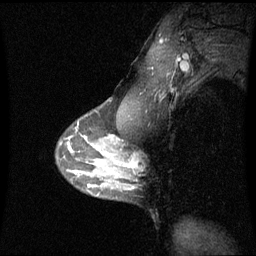
Breast MRI (dynamic contrast-enhanced), one sagittal slice; dynamic contrast-enhanced series, image 2 of 3 at this slice position (ordered by acquisition); 1.5 T; TE 4.2 ms, TR 8.9 ms; 256 × 256 image matrix, field of view 230 × 230 mm. Female patient, age 42 years. Case-level facts recorded for this patient, not image findings: setting: breast cancer imaged before/during neoadjuvant chemotherapy; receptor status: triple-negative.
Annotated regions visible in this slice (semi-automatic segmentation, software-assisted and operator-edited):
- analysis volume of interest (the breast-tissue region the enhancement analysis was run in; not a lesion): bounding box [x1, y1, x2, y2] px = [114, 150, 135, 180]
- tumour enhancement mask (voxels above the 70 % enhancement threshold inside the analysis volume of interest): [127, 159, 135, 168]